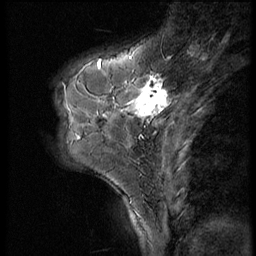
Breast MRI (dynamic contrast-enhanced), one sagittal slice. 3 images stored at this slice position (order not interpretable as contrast timing). 1.5 T. TE 4.2 ms, TR 9 ms. 2.5 mm slice thickness. 256 × 256 image matrix, field of view 180 × 180 mm. Female patient, age 46 years. From the clinical record (not read from this slice): setting: breast cancer imaged before/during neoadjuvant chemotherapy; receptor status: HER2-positive.
Annotated regions visible in this slice (semi-automatic segmentation, software-assisted and operator-edited):
- analysis volume of interest (the breast-tissue region the enhancement analysis was run in; not a lesion): bounding box <79,68,190,143> (left, top, right, bottom; pixels)
- tumour enhancement mask (voxels above the 140 % enhancement threshold inside the analysis volume of interest): <99,68,168,119>